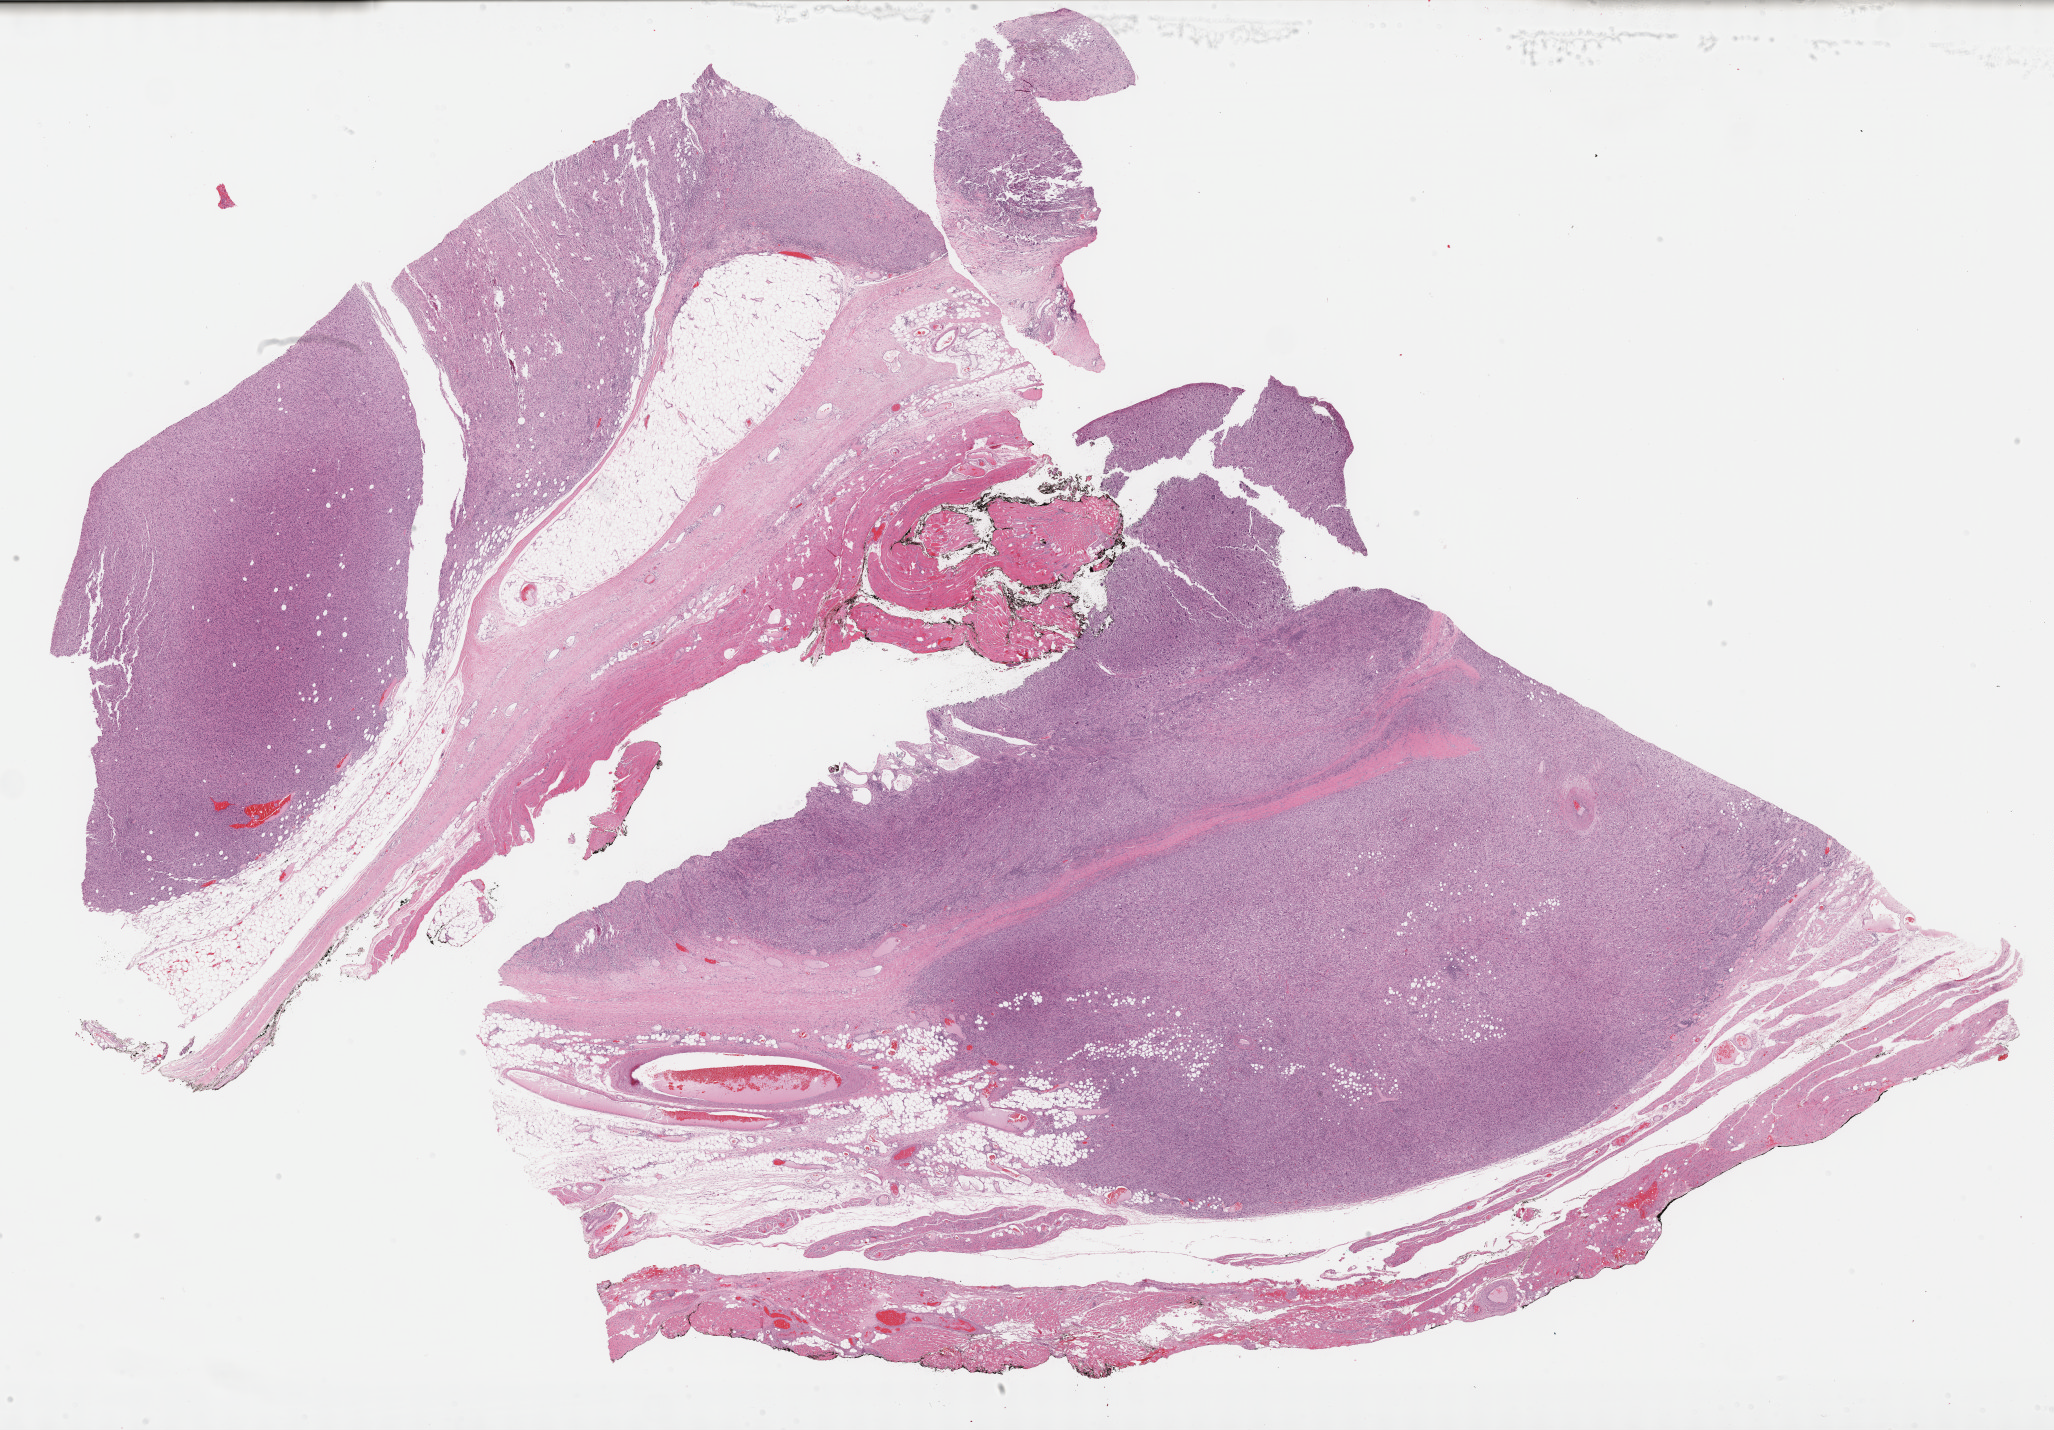
Whole-slide histology image, Hematoxylin and eosin (H&E) stained — low-resolution overview of the scanned area, about 33.2 x 23.1 mm, formalin-fixed paraffin-embedded (FFPE) diagnostic section, sample: primary tumour, connective, subcutaneous and other soft tissues. Female patient; age at initial diagnosis 65 years.
Pathologic diagnosis: Malignant fibrous histiocytoma (connective, subcutaneous and other soft tissues of lower limb and hip).